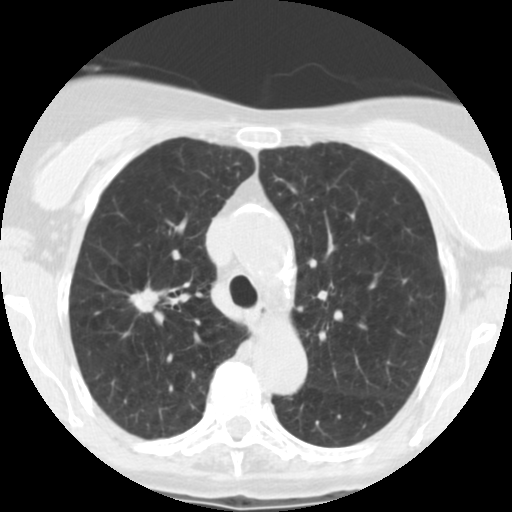
Low-dose screening chest CT, one axial slice. Slice 176 of 246 in the series (ordered by position). Lung window (W 1500 / L -600 HU). 2.5 mm slice thickness. 512 × 512 image matrix.
Structures marked on this image (outlined manually by an expert reader):
- lesion 1 (tumor, upper lobe of right lung): box from (x=129, y=286) to (x=159, y=313) px